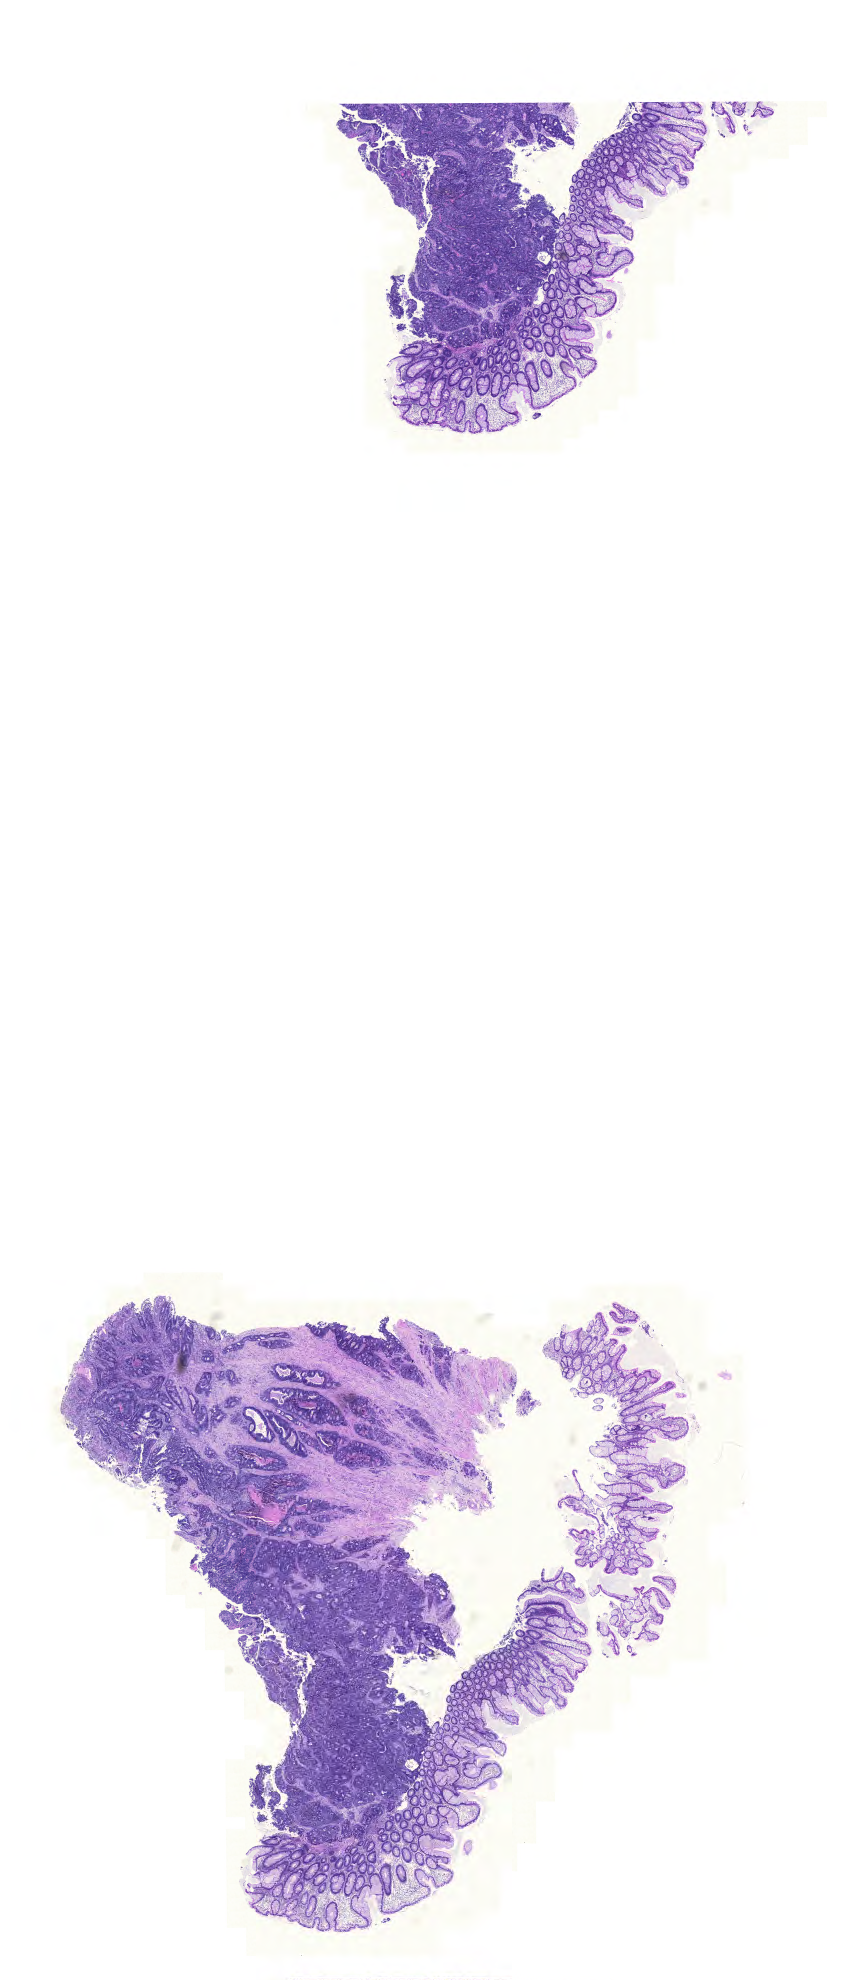
H&E whole-slide image — low-resolution overview of the scanned area, about 12.9 x 29.5 mm. FFPE section. Sample: primary tumour, rectum. Patient: female, age at initial diagnosis 61 years.
• lymph nodes positive (case pathology): 20 of 32 examined
• AJCC pathologic stage: IIIC (6th edition)
• histologic diagnosis: Adenocarcinoma, NOS (rectosigmoid junction)